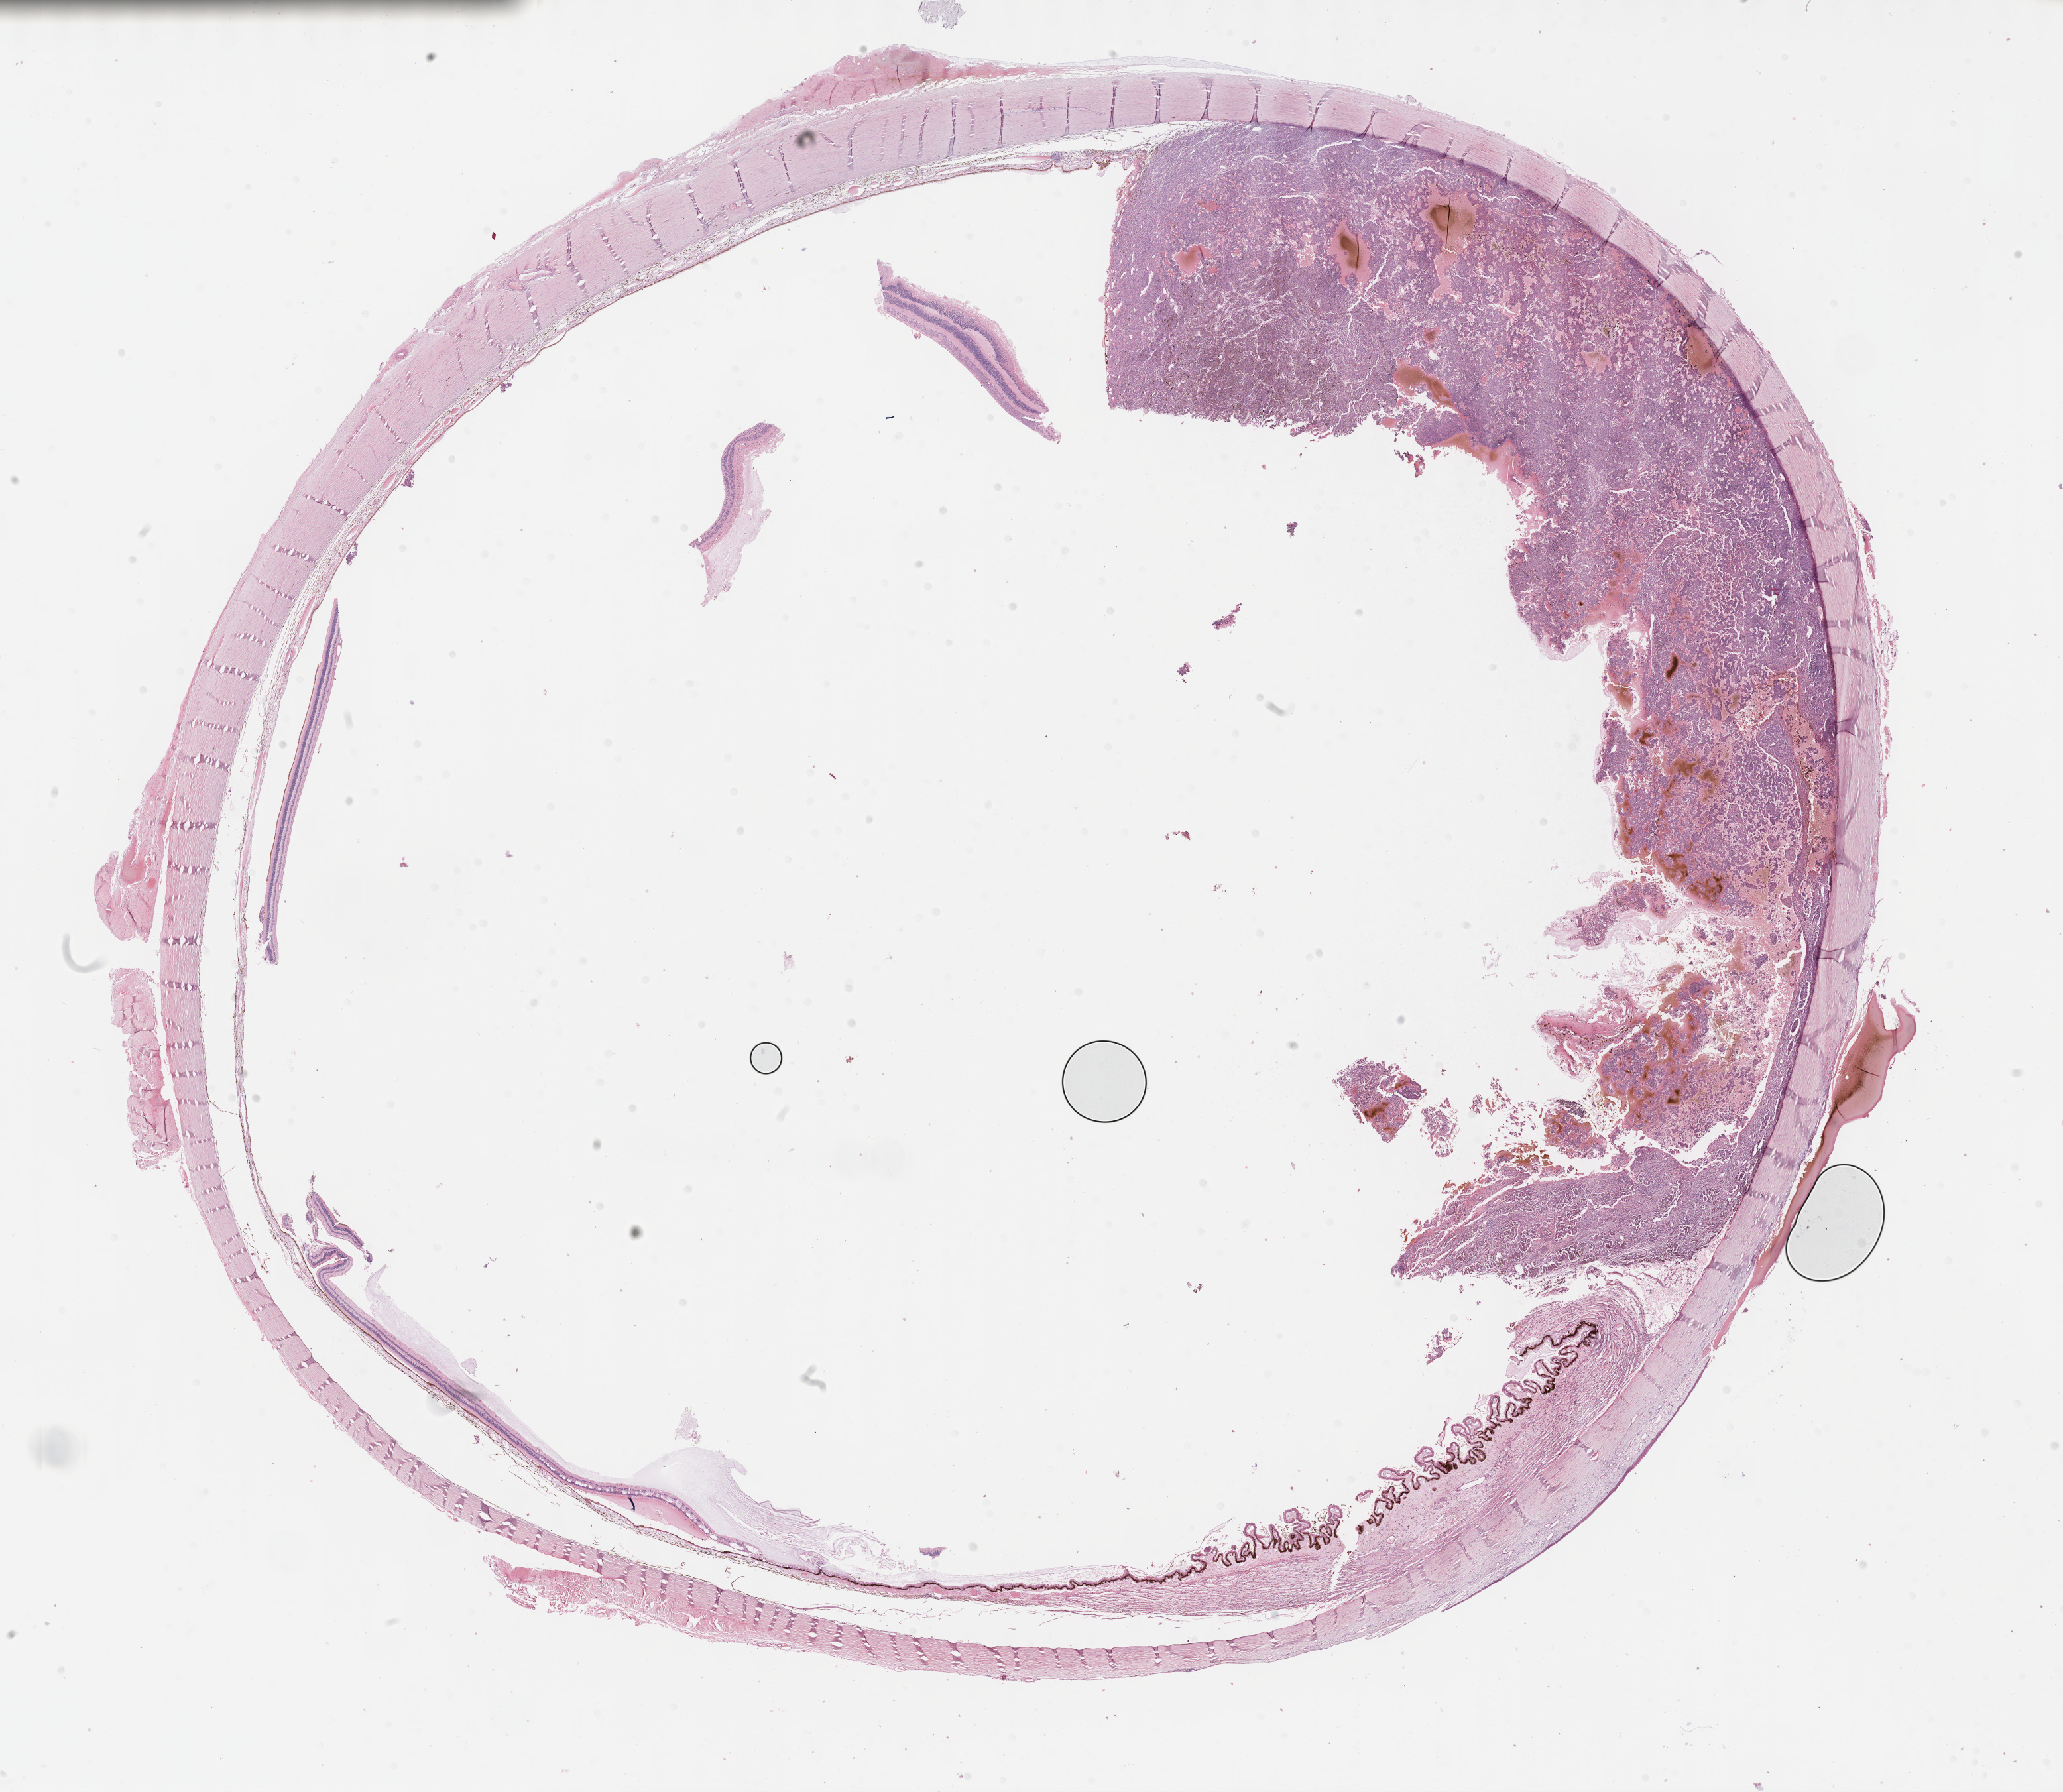
Whole-slide histology image, Hematoxylin and eosin (H&E) stained, a low-resolution overview of the entire scanned area, about 25.2 x 21.9 mm (from a 40x scan), formalin-fixed paraffin-embedded (FFPE) diagnostic section, uvea, primary tumour sample. Female patient; age at initial diagnosis 59 years.
TNM: T4a N0 M0. AJCC pathologic stage: IIIA. Laterality: right. Pathologic diagnosis: Mixed epithelioid and spindle cell melanoma (choroid).